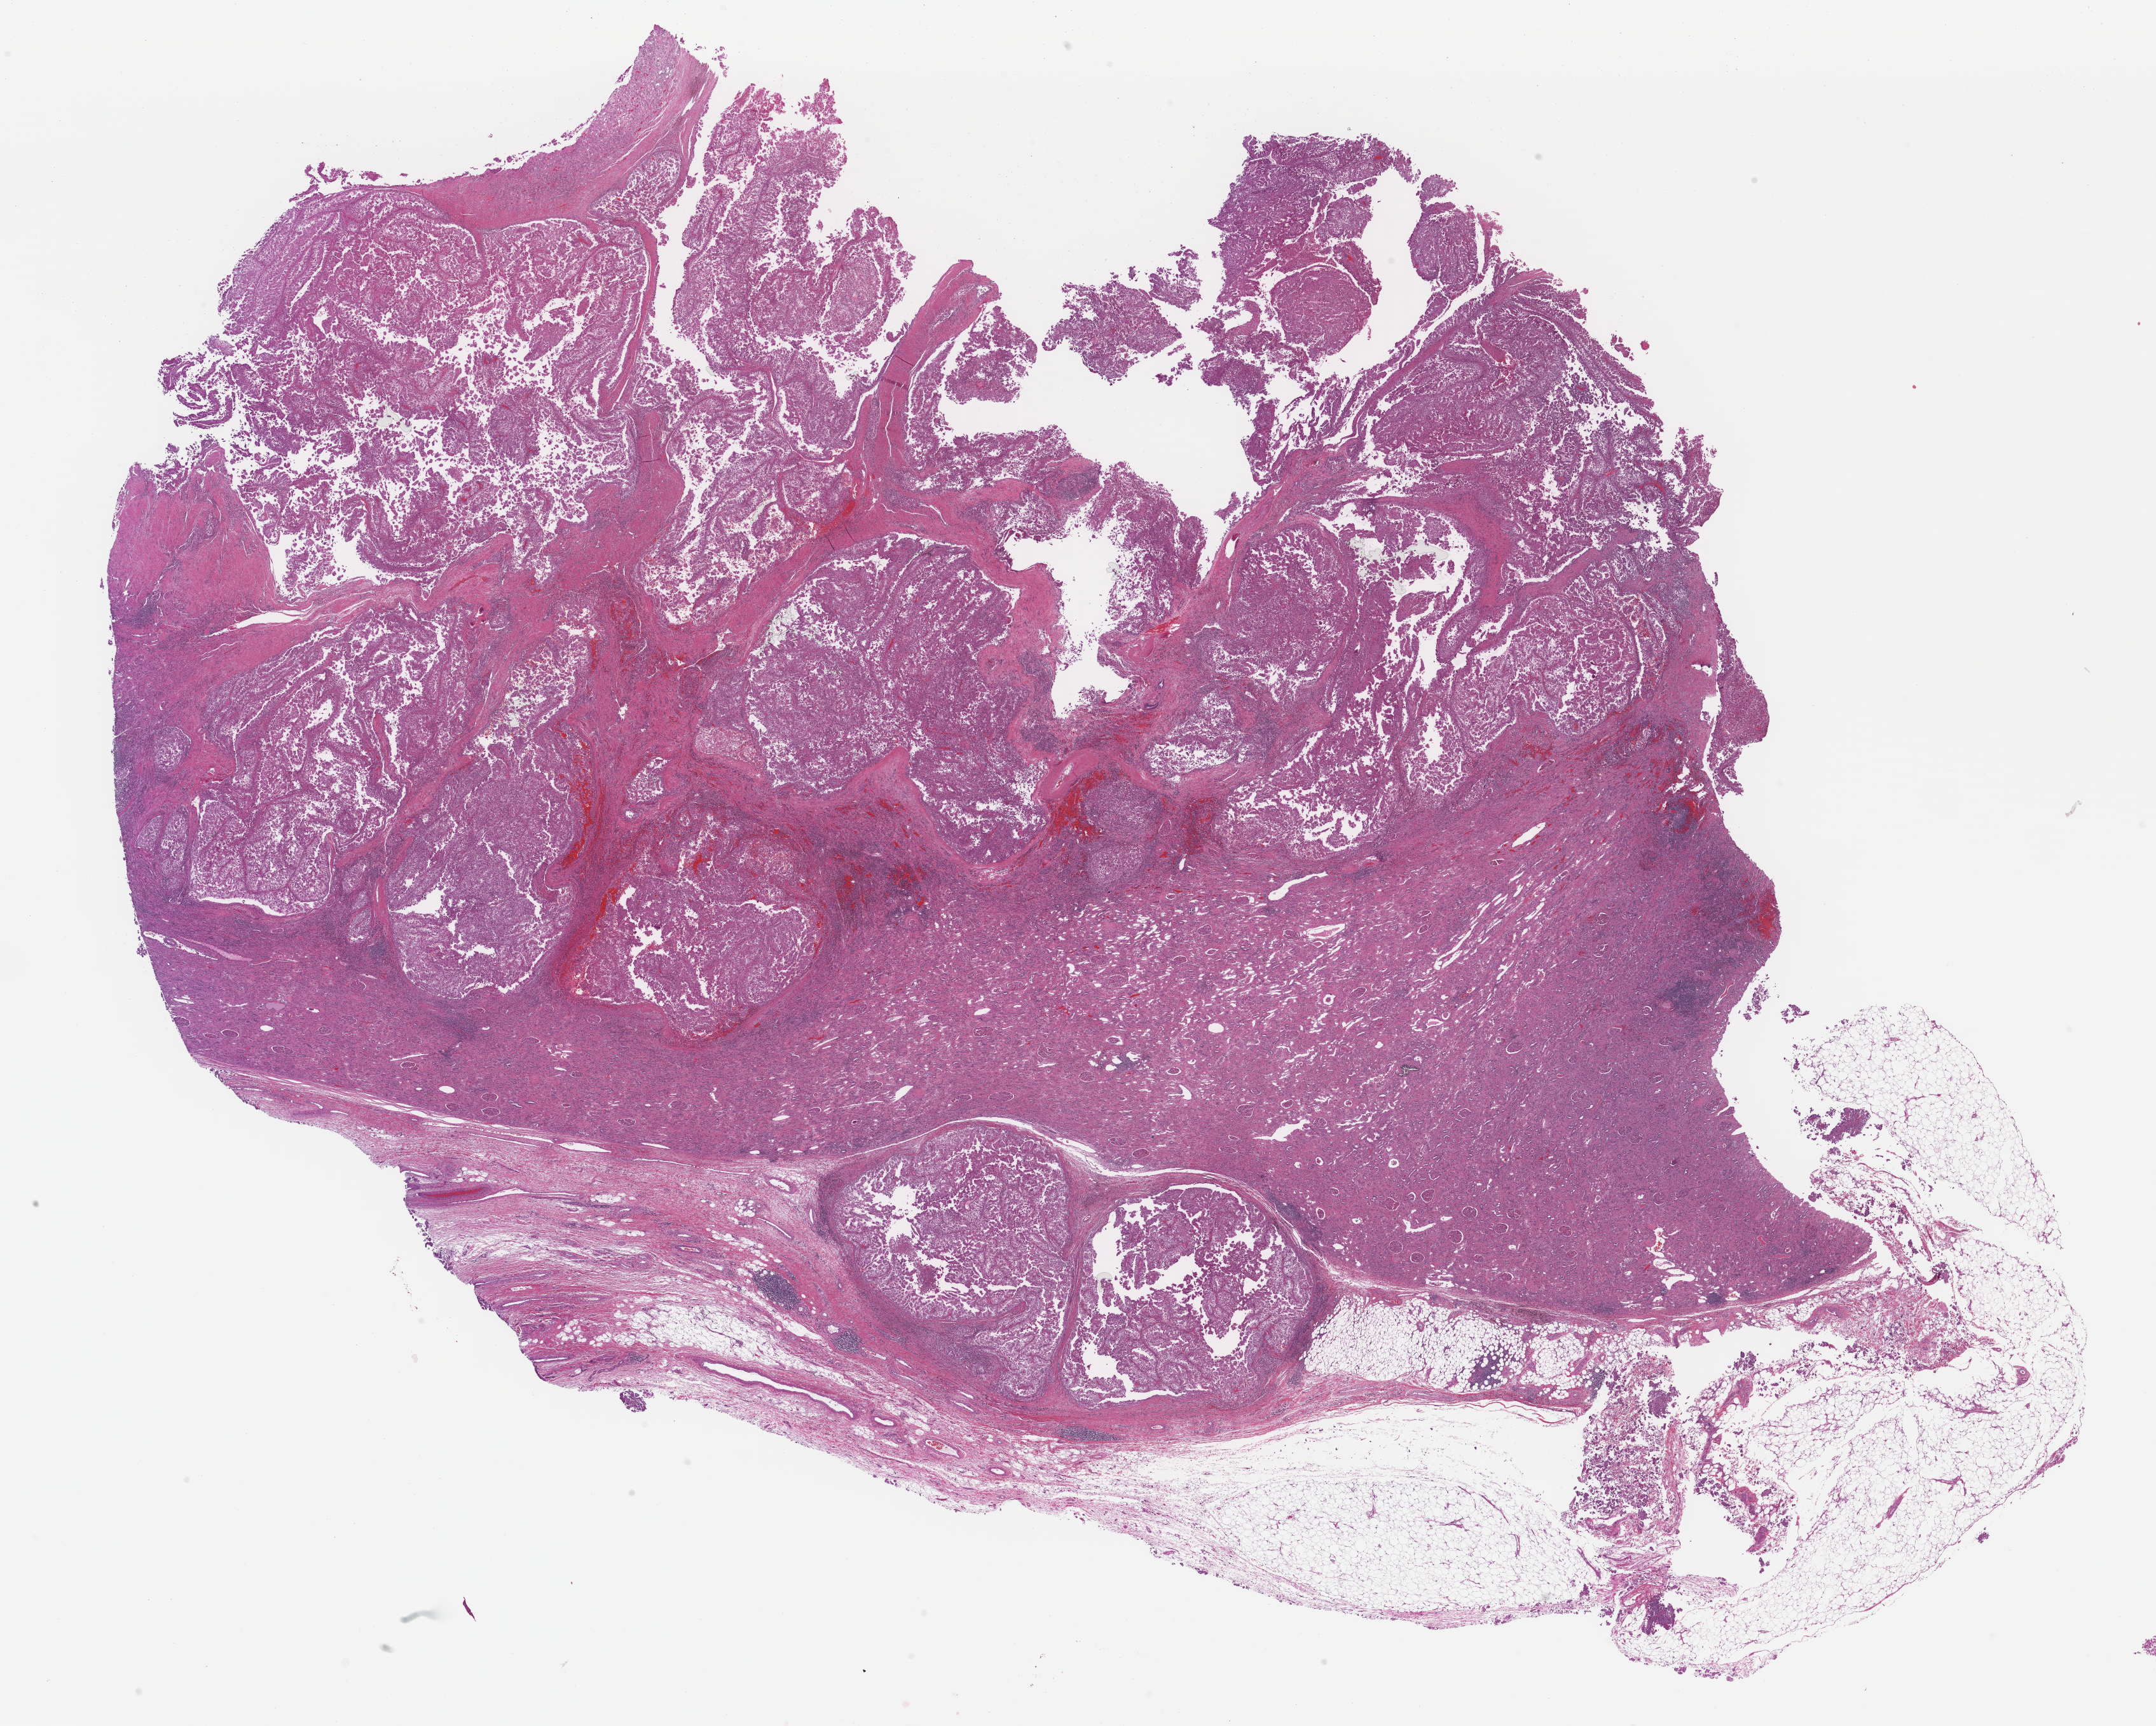
Whole-slide histology image, H&E — shown as a low-resolution overview of the whole scanned area (about 26.8 x 21.4 mm, acquisition: 40x scan), formalin-fixed paraffin-embedded (FFPE) diagnostic section, sample: primary tumour, kidney. Patient: male, age at initial diagnosis 59 years. Histologic grade: G4 (undifferentiated).
Histologic diagnosis: Clear cell adenocarcinoma, NOS. TNM: T3b N0 MX. AJCC pathologic stage: IV (6th edition).